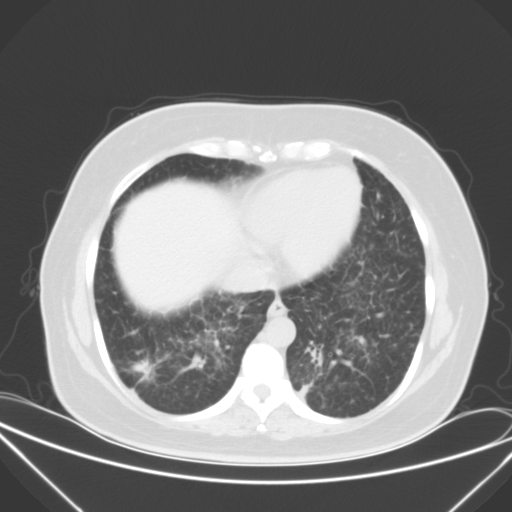
Chest CT, one axial slice; position 15 of 52 along the scan axis; lung window (W 1500 / L -600 HU); 5 mm slice thickness; 512 × 512 image matrix. Female patient, age 50 years. From the clinical record (not read from this slice): clinical TNM (as recorded): T1c N0 M1a.
Outlined on this slice (rectangle marked by the reading radiologist):
- lung tumour (recorded histology: adenocarcinoma): bounding box (x1, y1, x2, y2) in pixels: (128, 356, 166, 388)